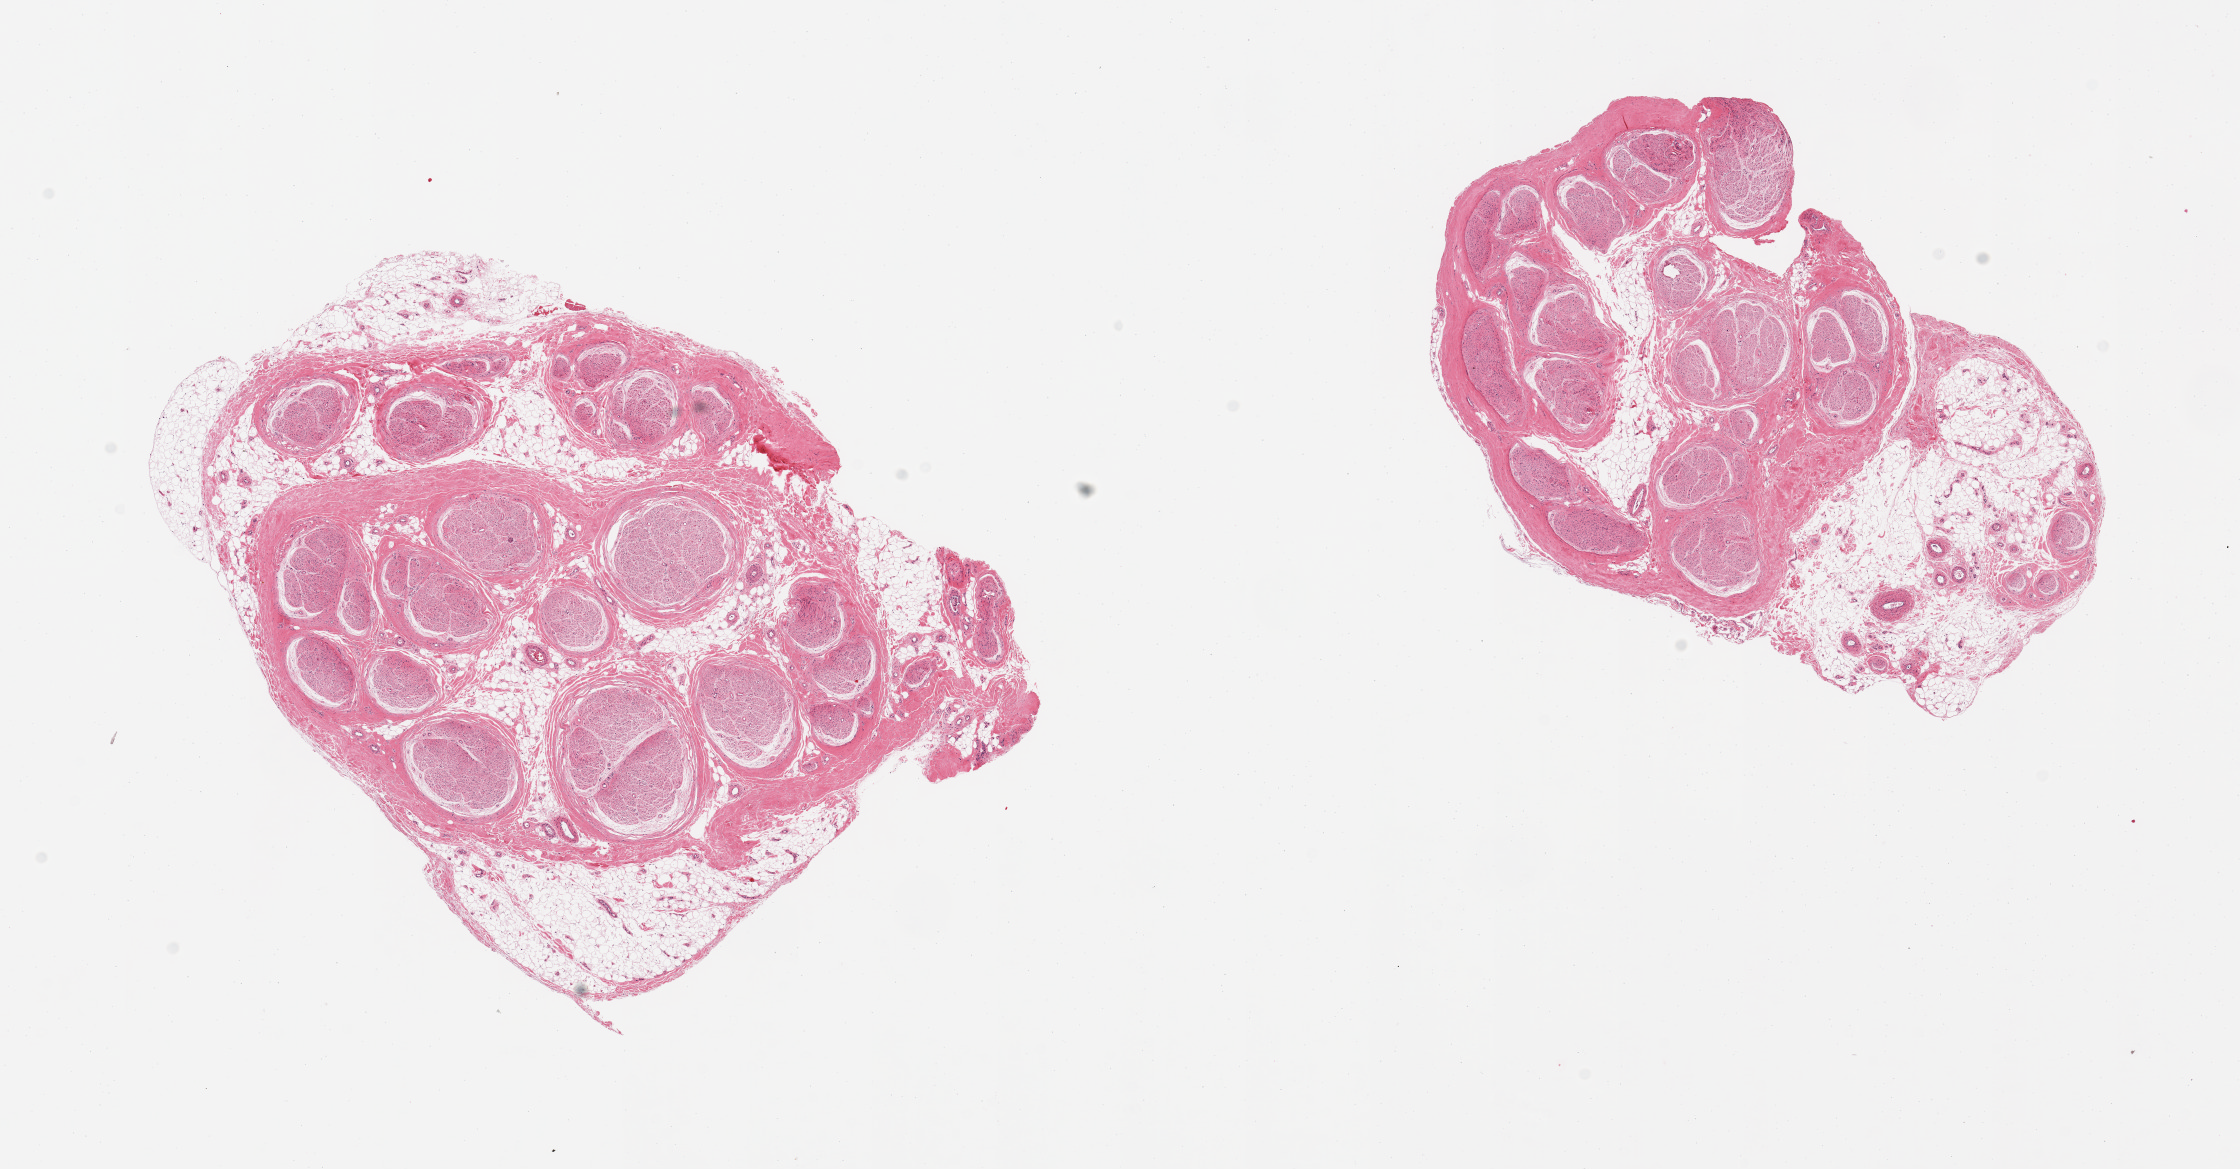
Whole-slide image, haematoxylin and eosin stain — shown as a low-resolution overview of the whole scanned area (about 17.7 x 9.2 mm); PAXgene-fixed, paraffin-embedded tissue; target tissue: tibial nerve; donor tissue sample. Donor: male.
- pathologist's review note for this sample: 2 pieces, nubbins adherent fat up to 2 mm